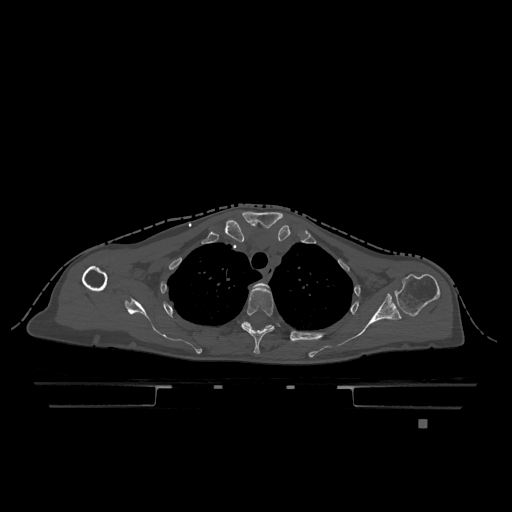
CT including the spine, one axial slice. Position 917 of 1317 along the scan axis. Bone window (W 1800 / L 400 HU). 0.5 mm slice thickness. 512 × 512 image matrix. Patient: female, 74 years. Case-level facts recorded for this patient, not image findings: primary cancer: lung.
Annotated regions visible in this slice (semi-automatically segmented with operator editing):
- T2 vertebra: box from (x=252, y=282) to (x=269, y=290) px
- T3 vertebra: (x=241, y=286)–(x=275, y=354)
- T4 vertebra: (x=243, y=322)–(x=307, y=342)